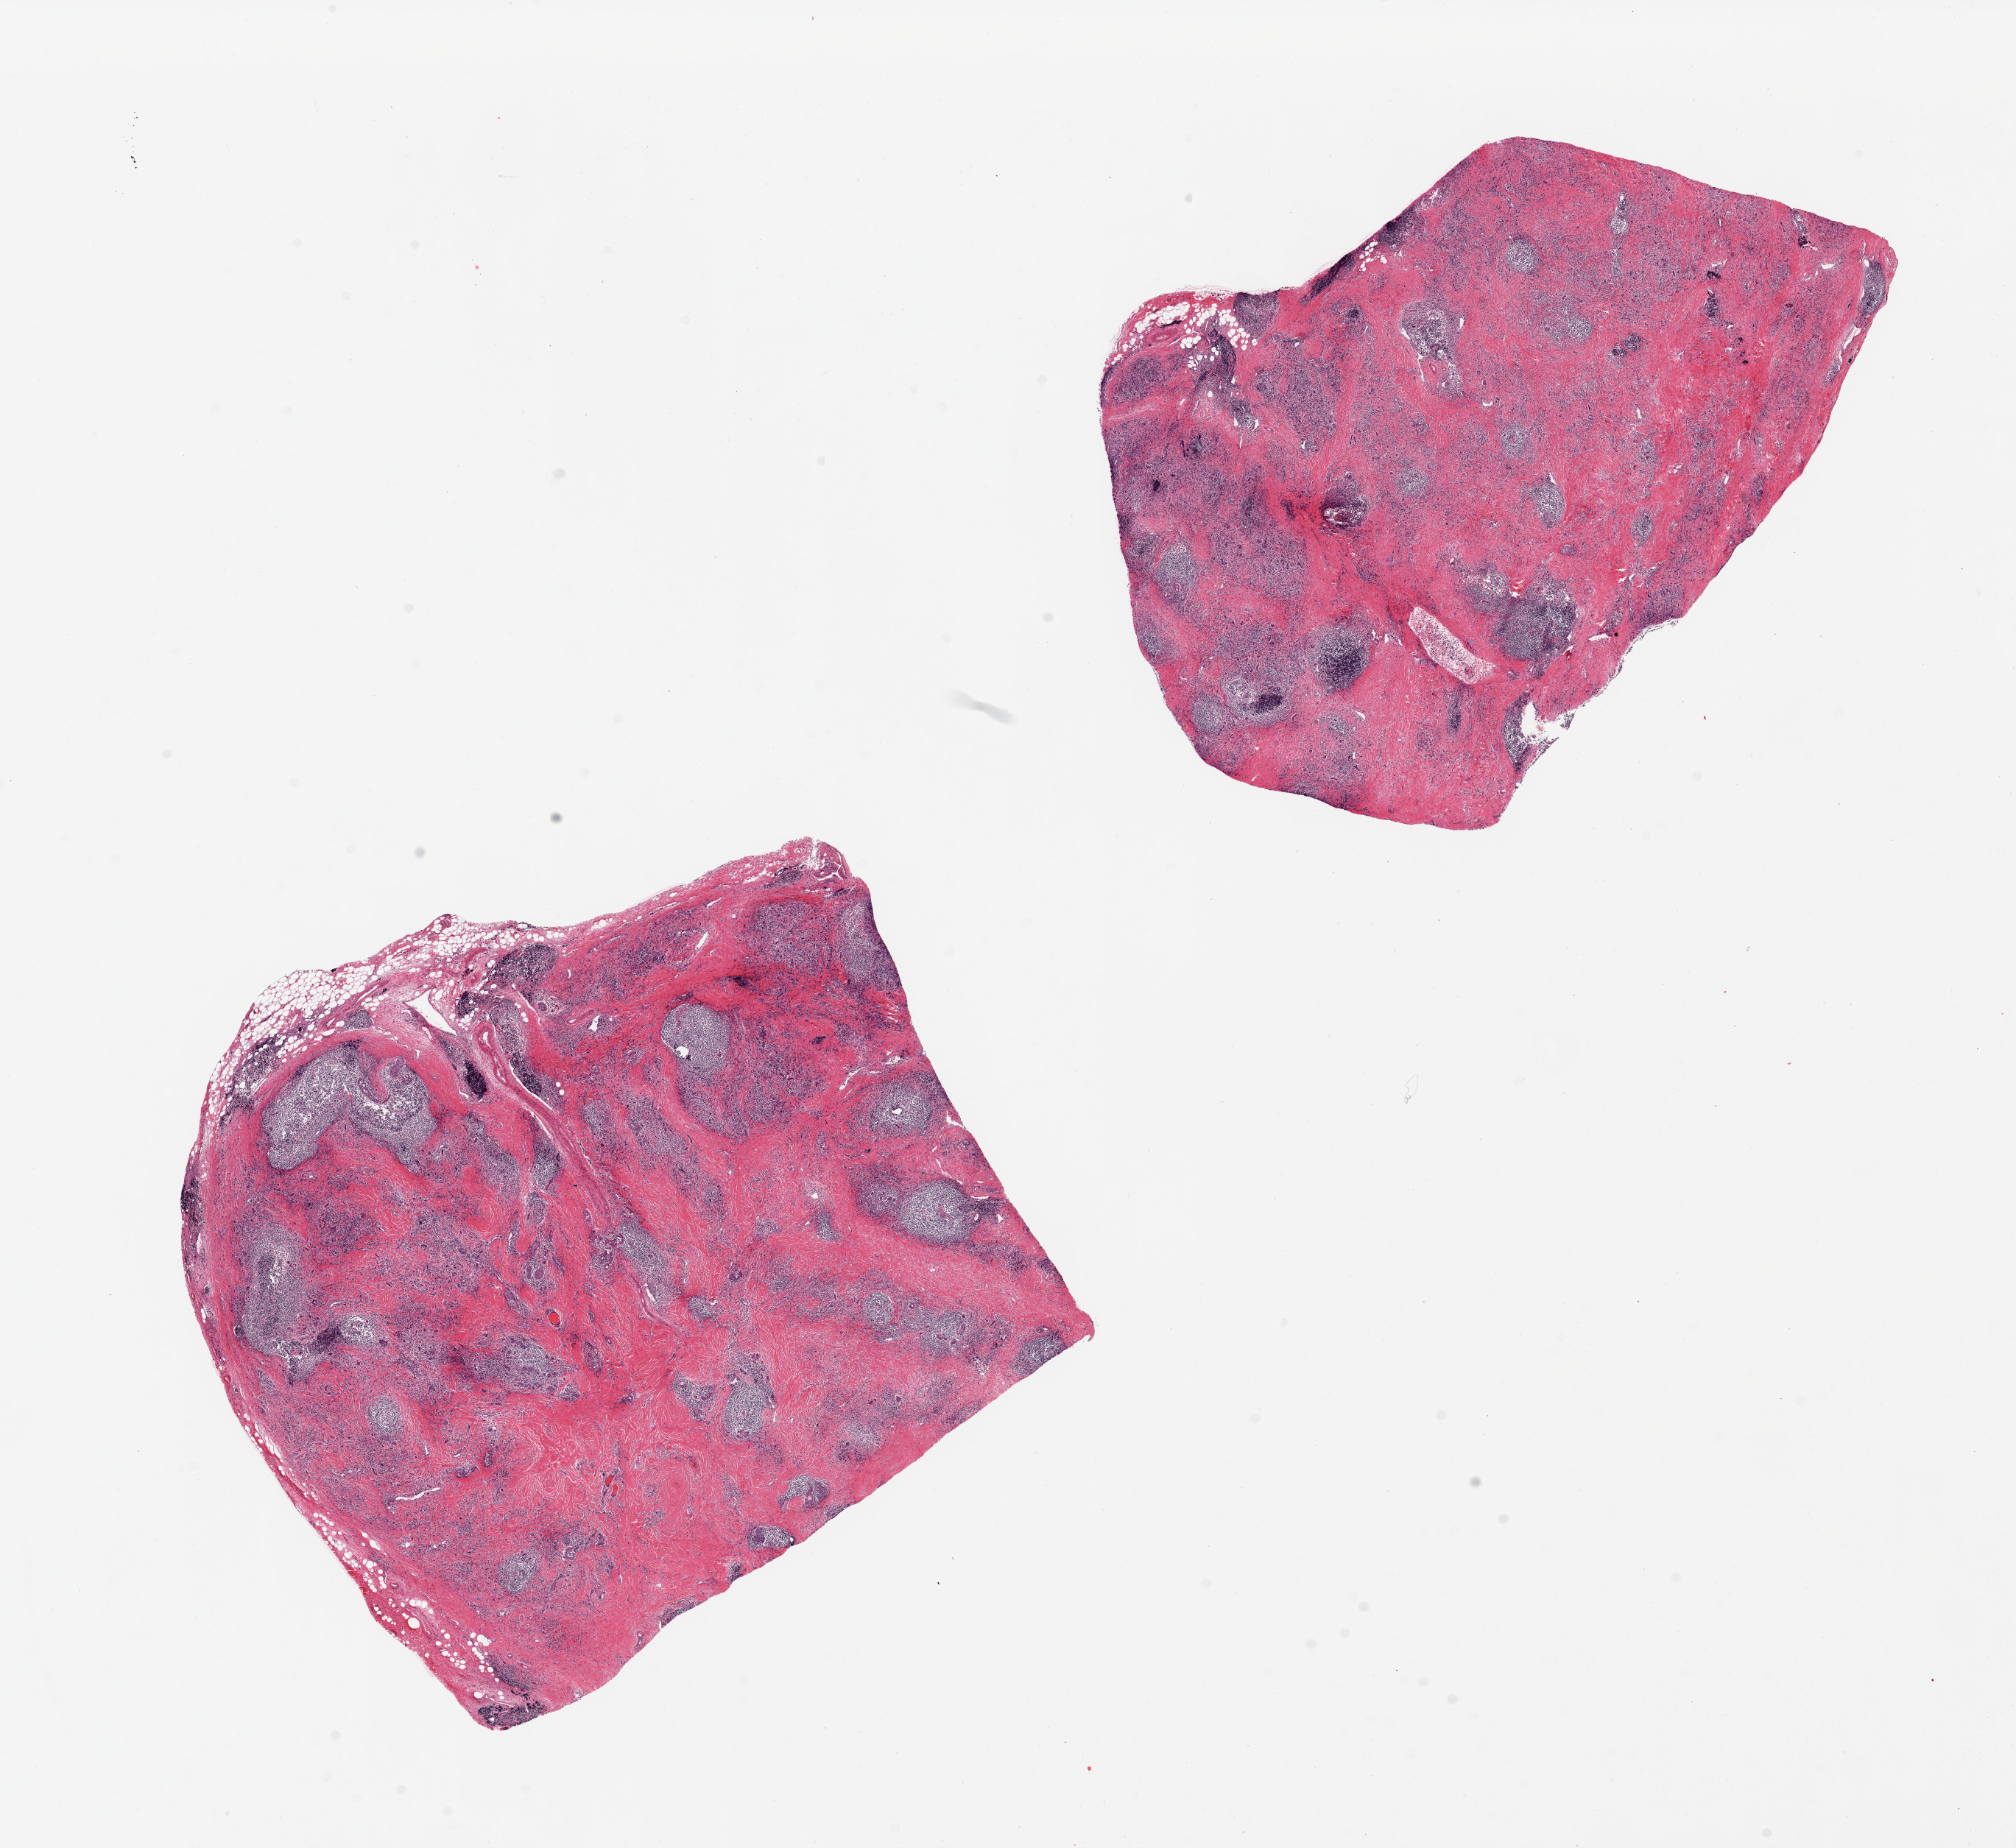
Digitized H&E-stained section, low-resolution overview of the scanned area, about 21.7 x 19.9 mm. PAXgene-fixed paraffin-embedded (PFPE) section. Section of thyroid (target tissue). Donor tissue sample.
Reviewer comment on this tissue sample: 2 pieces, 8x8 and 9x6mm; end-stage Hashimoto's thyroiditis, dense fibrous scarrning and numerous lymphoid follicles.